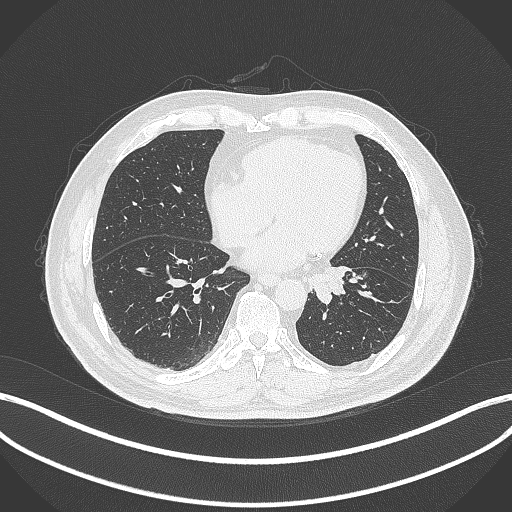
Chest CT, one axial slice. Position 95 of 312 along the scan axis. Reconstruction kernel B70f. Lung window (W 1500 / L -600 HU). 1 mm slice thickness. 512 × 512 image matrix, field of view 400 × 400 mm. Male patient, age 71 years. Case-level facts recorded for this patient, not image findings: clinical TNM (as recorded): T1b N0 M0.
Outlined on this slice (bounding box drawn by a radiologist):
- lung tumour (recorded histology: squamous cell carcinoma): bounding box [x1, y1, x2, y2] px = [308, 266, 357, 304]